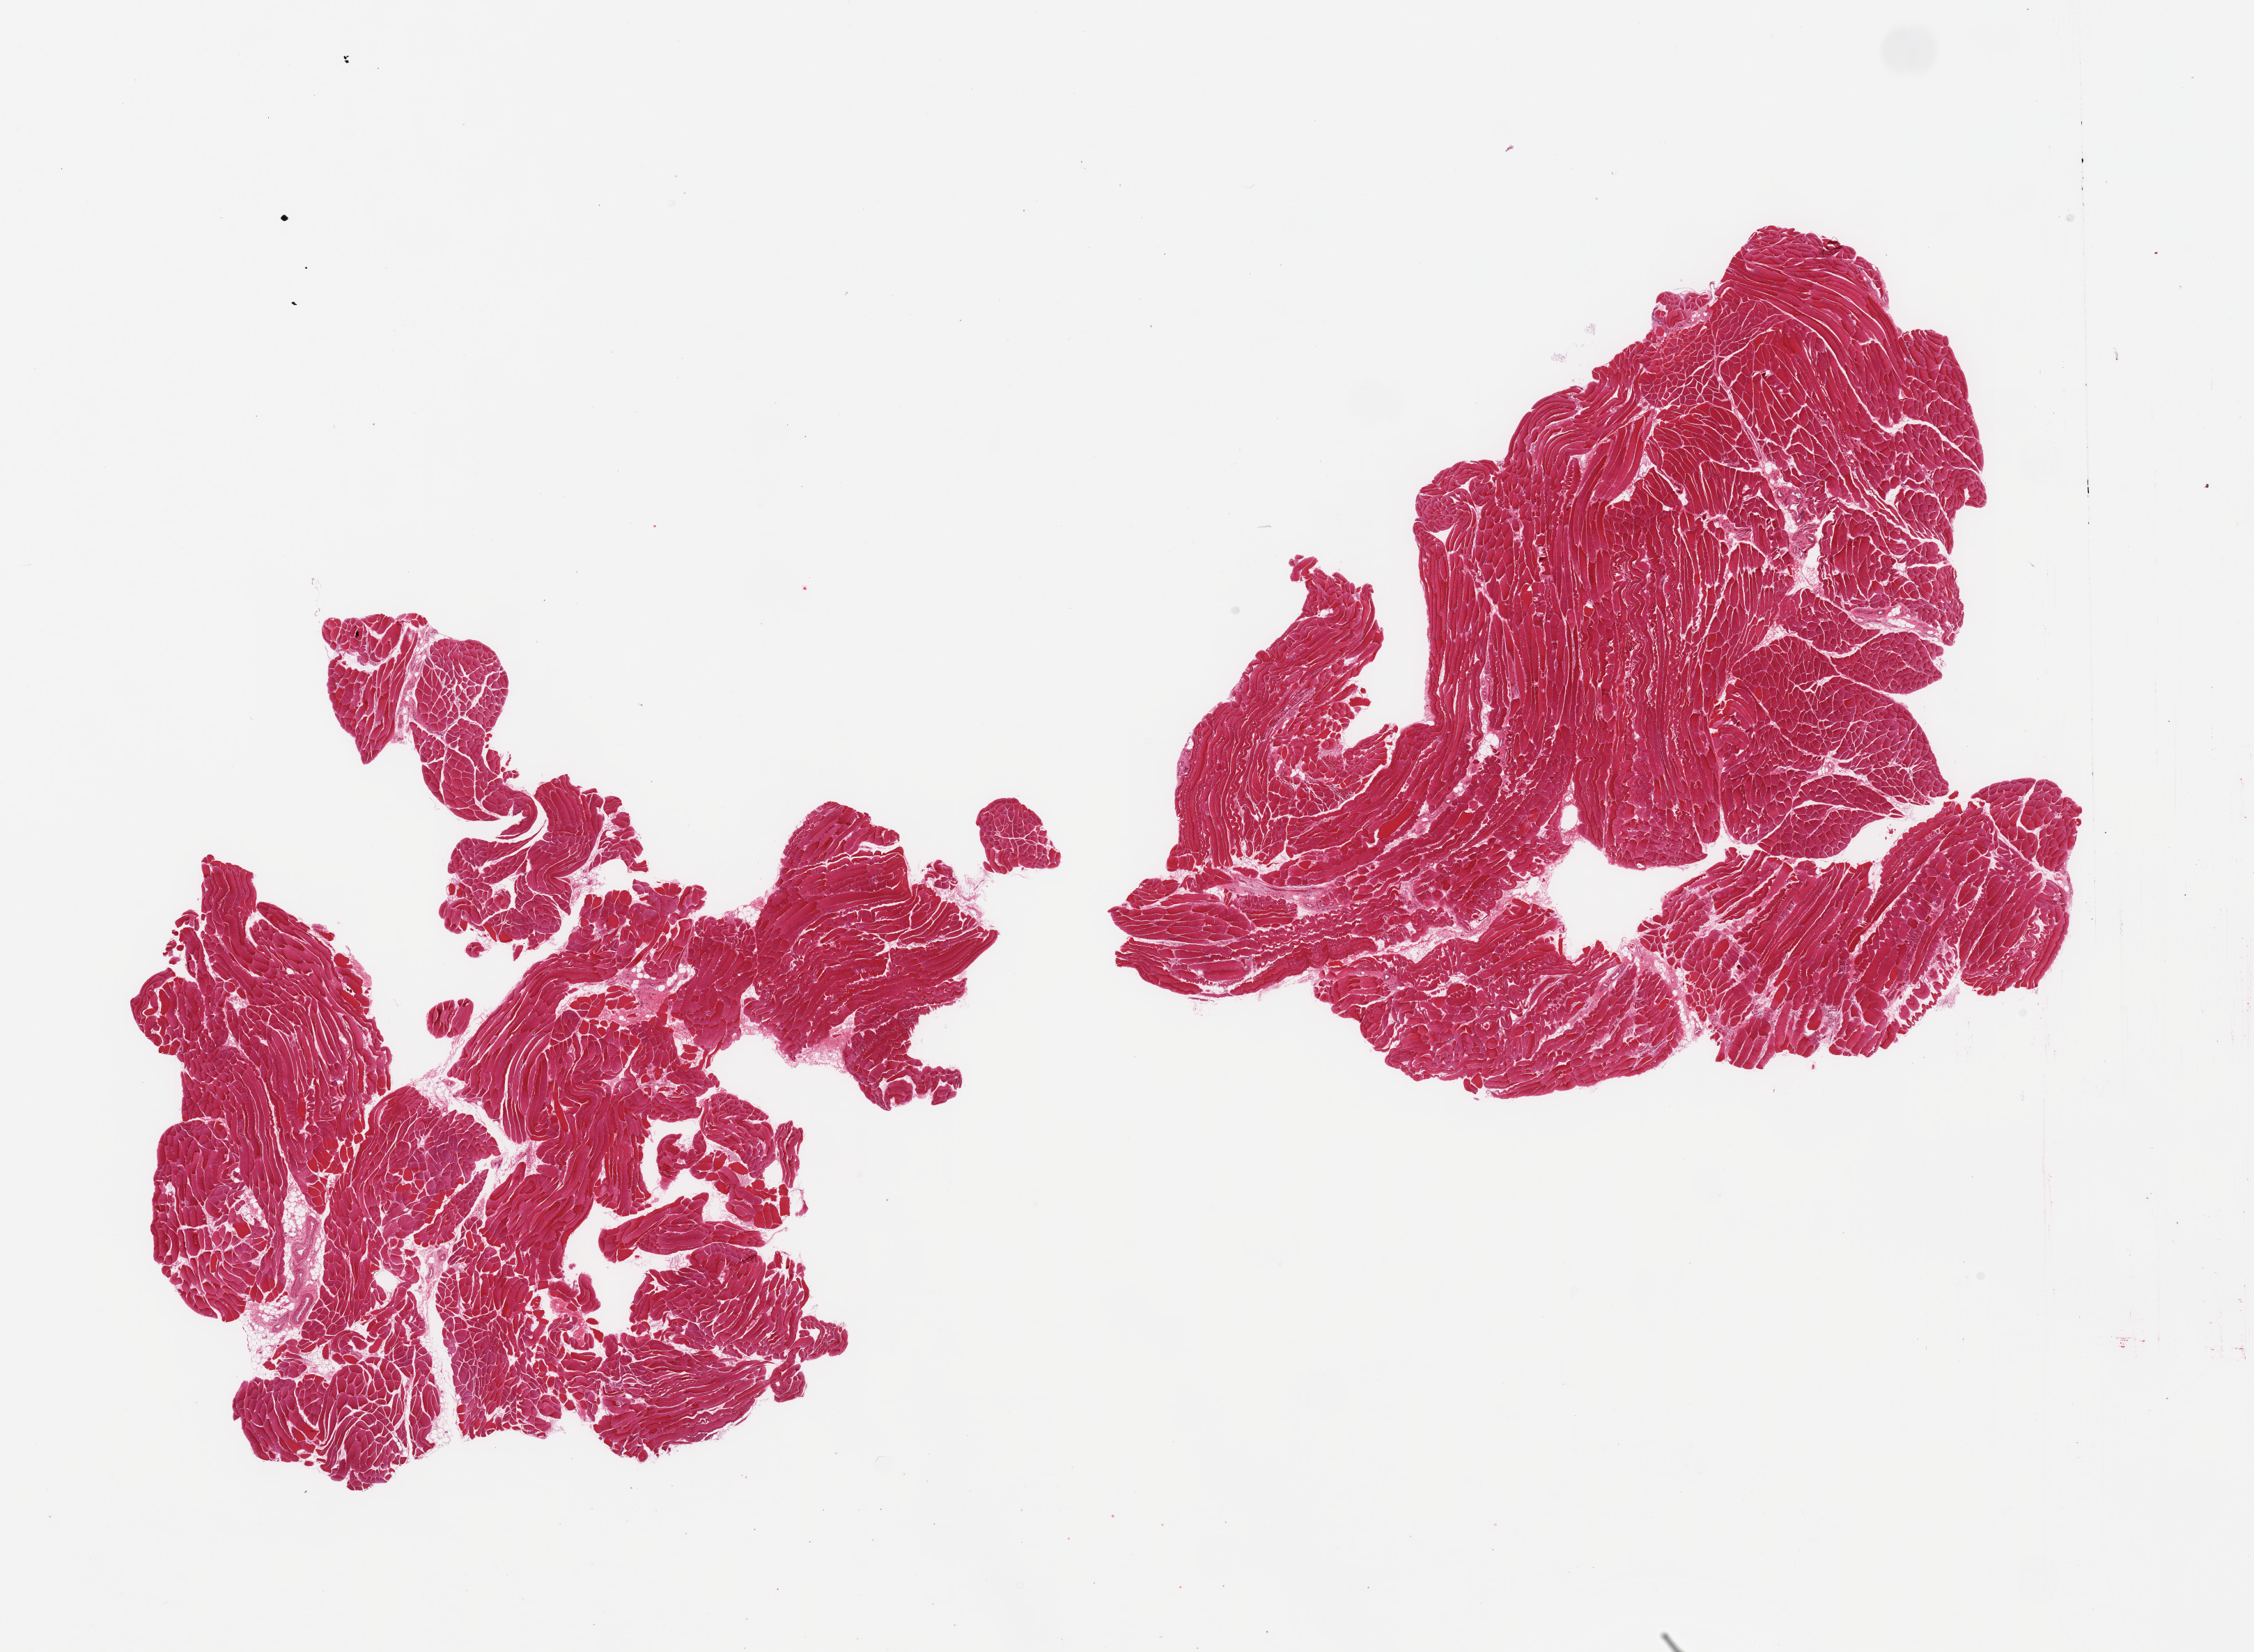
Haematoxylin and eosin whole-slide image, brightfield, low-resolution overview of the scanned area, about 25.6 x 18.8 mm (slide scanned at 20x); PAXgene-fixed paraffin-embedded (PFPE) section; target tissue: skeletal muscle; tissue donor sample. Donor: male.
- reviewer comment on this tissue sample: 2 pieces, trace interstitial fat